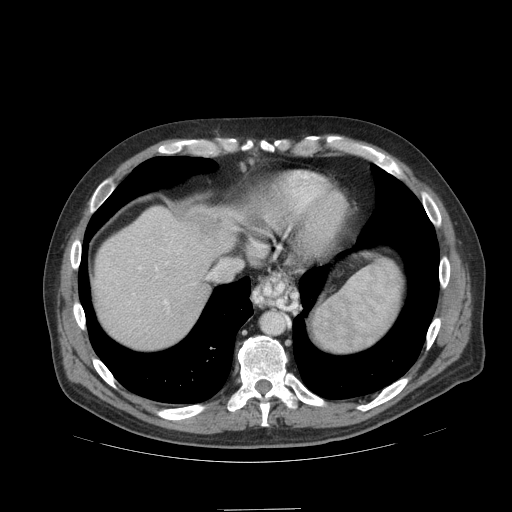
Contrast-enhanced abdominal CT (liver protocol), one axial slice; position 88 of 99 along the scan axis; reconstruction kernel STANDARD; 140 kVp; soft-tissue window (W 400 / L 40 HU); 2.5 mm slice thickness; 512 × 512 image matrix, field of view 440 × 440 mm. From the clinical record (not read from this slice): diagnosis: hepatocellular carcinoma (patient treated with transarterial chemoembolisation; whether this scan precedes or follows treatment is not stated here); TNM stage (as recorded): Stage-I; Child-Pugh class: A; tumour differentiation: no biopsy; tumour nodularity: uninodular.
Outlined on this slice (semi-automatically segmented with operator editing):
- abdominal aorta: bounding box [x1, y1, x2, y2] px = [262, 314, 284, 334]
- liver parenchyma outside the tumour (the mass and vessels are separate outlines, so this box may not span the whole liver): [94, 206, 242, 348]
- mass: [191, 212, 224, 249]
- liver vessels: [128, 246, 181, 305]